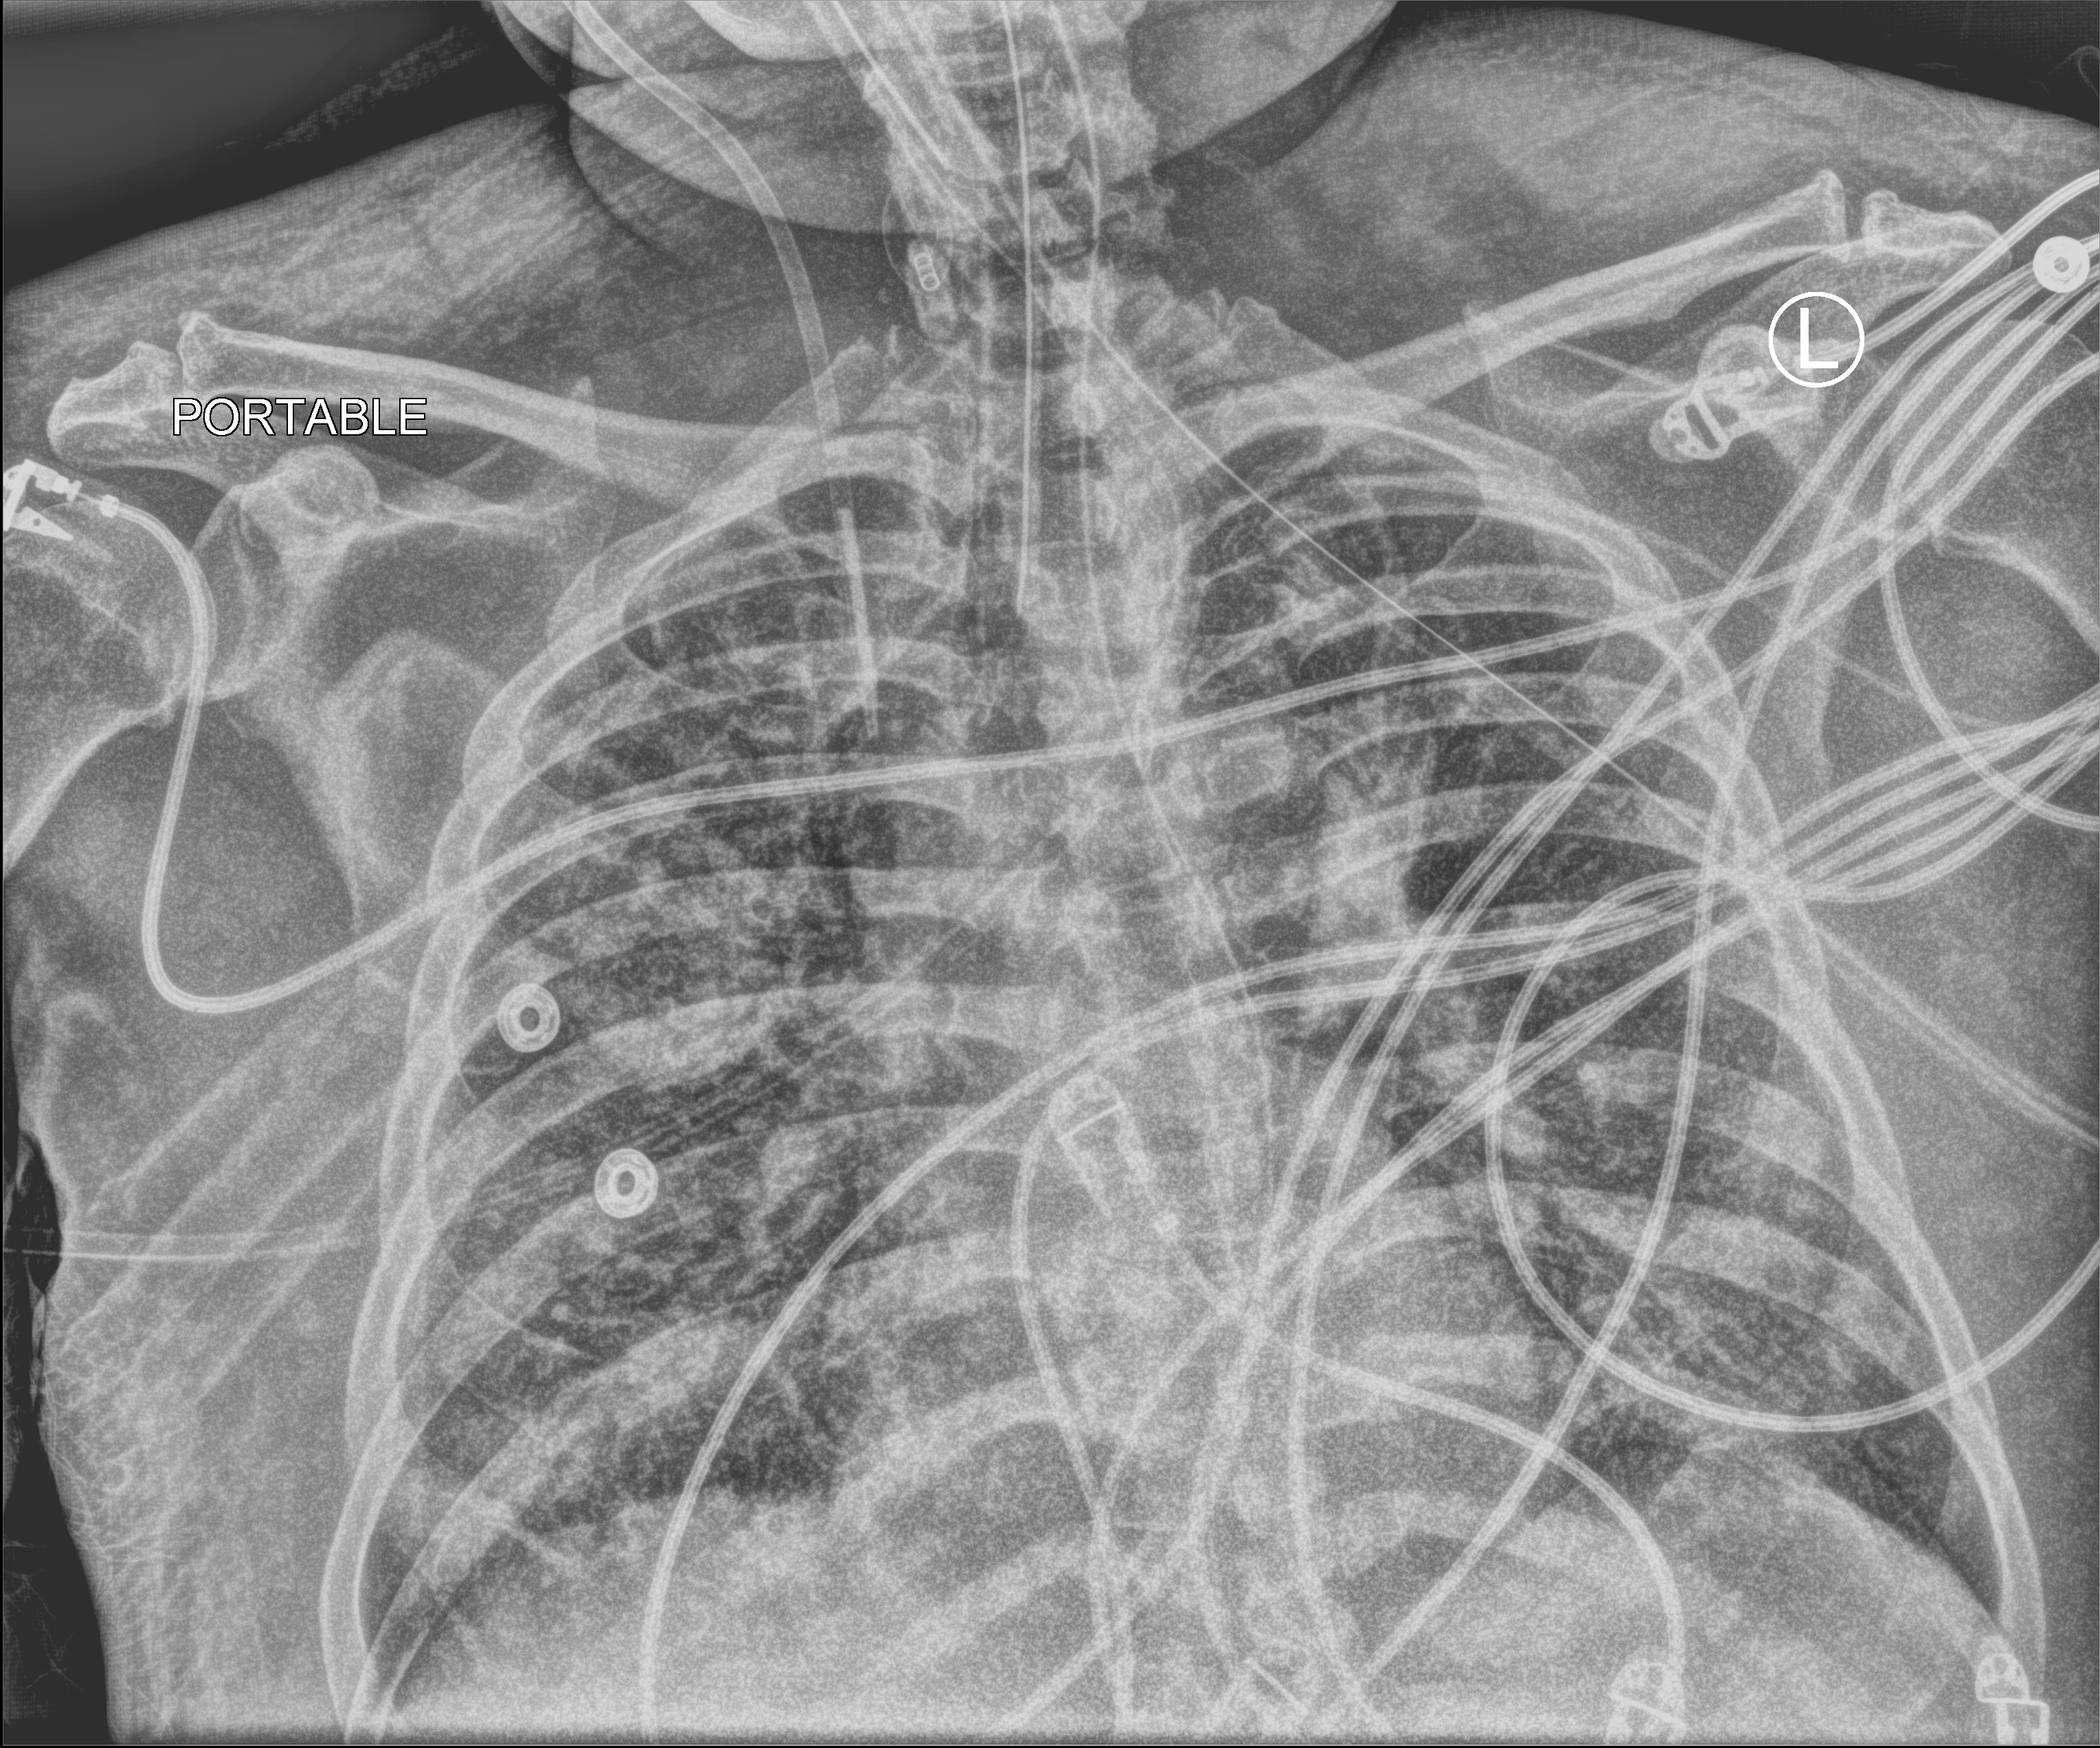
Bedside chest radiograph (computed radiography); anteroposterior (AP) projection. Patient hospitalised with COVID-19; male, aged 60–74 years.
Admission-level facts for this patient (not findings on this image; timing relative to this image not recorded): other chronic lung disease (admission record): no; admitted to intensive care during this hospital stay: yes; mechanically ventilated during this hospital stay: yes.